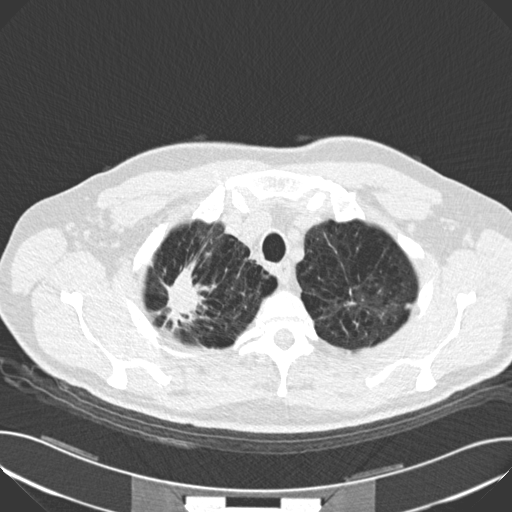
Low-dose screening chest CT, one axial slice. Position 140 of 159 along the scan axis. Reconstruction kernel B30f. 120 kVp. Lung window (W 1500 / L -600 HU). 2 mm slice thickness. 512 × 512 image matrix, field of view 380 × 380 mm.
Annotated regions visible in this slice (expert manual segmentation):
- lesion 1 (tumor, upper lobe of right lung): bounding box [x1, y1, x2, y2] px = [166, 268, 202, 318]